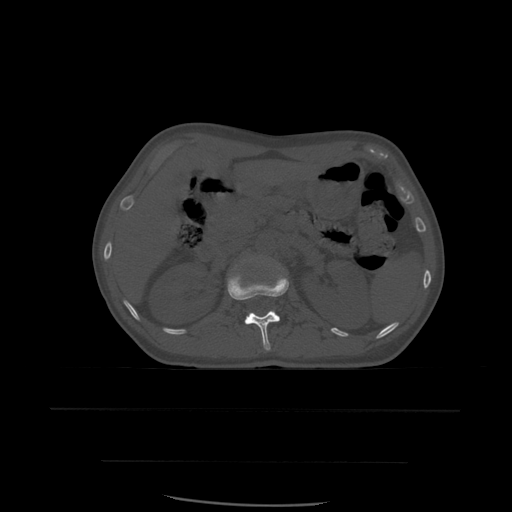
CT including the spine, one axial slice; position 245 of 574 along the scan axis; bone window (W 1800 / L 400 HU); 1.25 mm slice thickness; 512 × 512 image matrix, field of view 392 × 392 mm. Patient age 48 years. Case-level facts recorded for this patient, not image findings: primary cancer: lung; vertebrae with lytic lesions (as recorded): T11.
Annotated regions visible in this slice (semi-automatically segmented with operator editing):
- L1 vertebra: bounding box (x1, y1, x2, y2) in pixels: (227, 265, 289, 351)